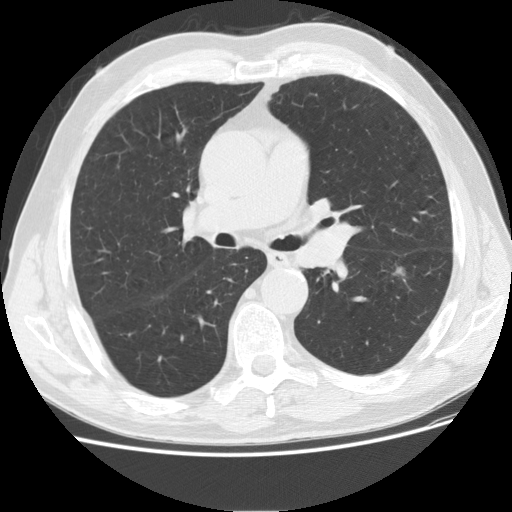
Low-dose screening chest CT, one axial slice; position 108 of 175 along the scan axis; 120 kVp; lung window (W 1500 / L -600 HU); 512 × 512 image matrix.
Outlined on this slice (outlined manually by an expert reader):
- lesion 1 (tumor, lower lobe of left lung): bounding box <392,265,406,276> (left, top, right, bottom; pixels)